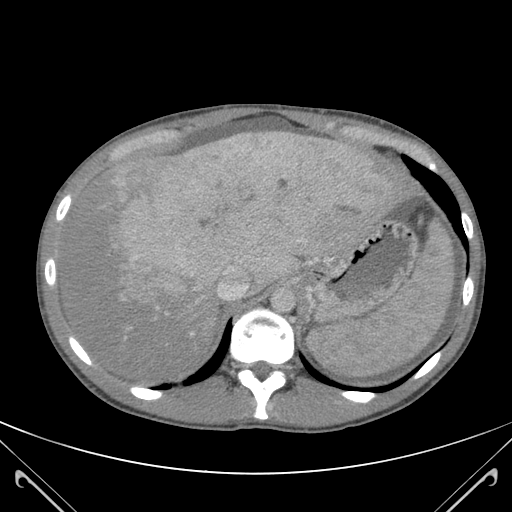
Contrast-enhanced abdominal CT (liver protocol), one axial slice. Position 92 of 118 along the scan axis. 120 kVp. Soft-tissue window (W 400 / L 40 HU). 3 mm slice thickness. 512 × 512 image matrix. From the clinical record (not read from this slice): diagnosis: hepatocellular carcinoma (patient treated with transarterial chemoembolisation; whether this scan precedes or follows treatment is not stated here); TNM stage (as recorded): Stage-IIIB; Child-Pugh class: A.
Outlined on this slice (semi-automatic segmentation, software-assisted and operator-edited):
- abdominal aorta: bounding box [x1, y1, x2, y2] px = [273, 288, 296, 312]
- liver parenchyma outside the tumour (the mass and vessels are separate outlines, so this box may not span the whole liver): [62, 130, 422, 378]
- mass: [99, 131, 398, 310]
- liver vessels: [191, 146, 342, 335]